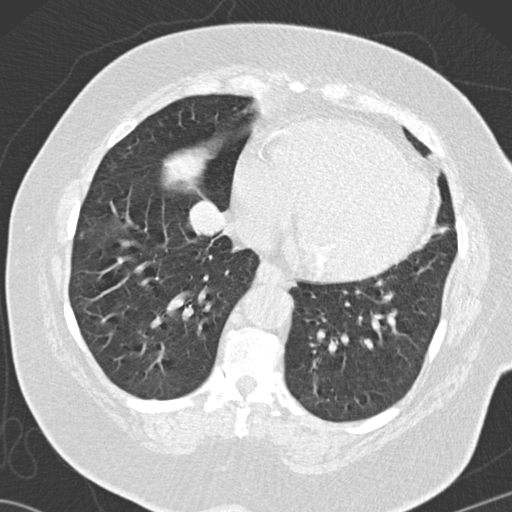
Low-dose screening chest CT, one axial slice. Position 48 of 146 along the scan axis. Reconstruction kernel B30f. 120 kVp. Lung window (W 1500 / L -600 HU). 2 mm slice thickness. 512 × 512 image matrix, field of view 350 × 350 mm.
Outlined on this slice (expert manual segmentation):
- lesion 3 (tumor, lower lobe of right lung): bounding box (x1, y1, x2, y2) in pixels: (187, 200, 227, 238)